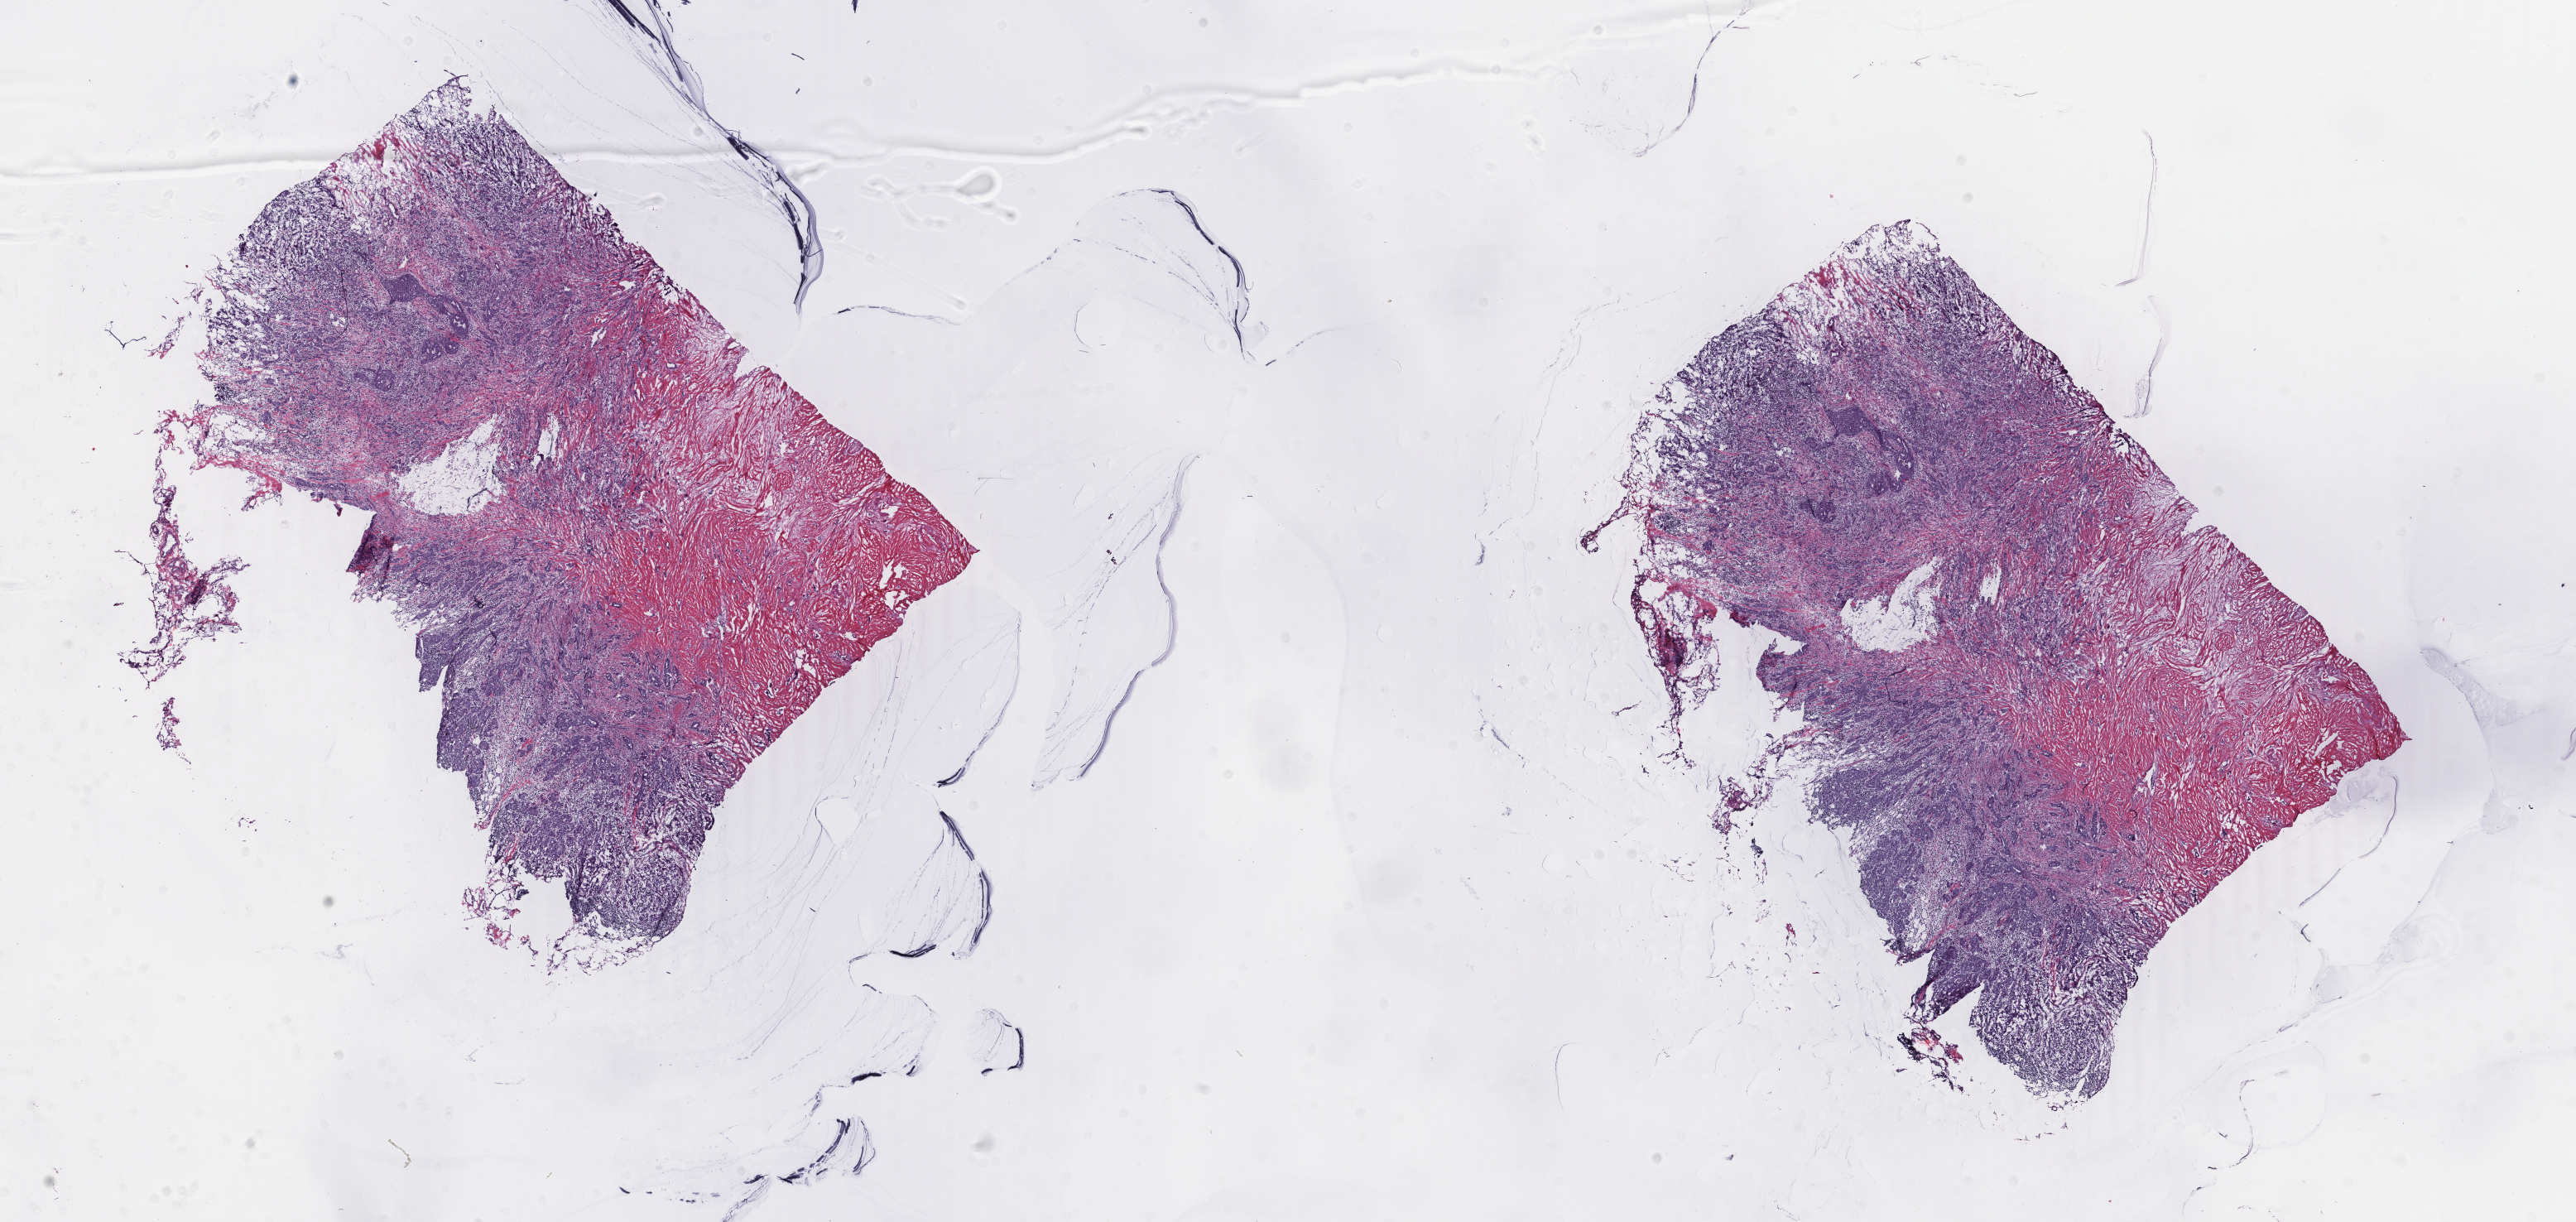
Whole-slide histology image, Hematoxylin and eosin (H&E) stained — shown as a low-resolution overview of the whole scanned area (about 24.7 x 11.7 mm); frozen section from the top of the tissue portion; sample: primary tumour, breast. Female patient; age at initial diagnosis 40 years. Composition of this section per pathologist review: tumour cells 60%, tumour nuclei 60%, normal cells 0%, stromal cells 40%, necrosis 0%. Infiltration values recorded for this section: lymphocyte infiltration 50%, monocyte infiltration 20%, neutrophil infiltration 20%.
* diagnosis: Infiltrating duct carcinoma, NOS
* lymph nodes positive (case pathology): 1 of 15 examined